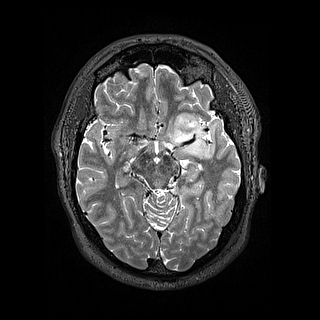
Brain MRI from a brain-tumour surgery series, one axial slice; position 94 of 144 along the scan axis; 320 × 320 image matrix, field of view 254 × 254 mm. From the clinical record (not read from this slice): histopathology: Astrocytoma; WHO grade: 2; IDH mutation: yes; tumour location: Left Insular.
Outlined on this slice (manually delineated by an expert):
- tumour: bounding box [x1, y1, x2, y2] px = [172, 110, 207, 157]